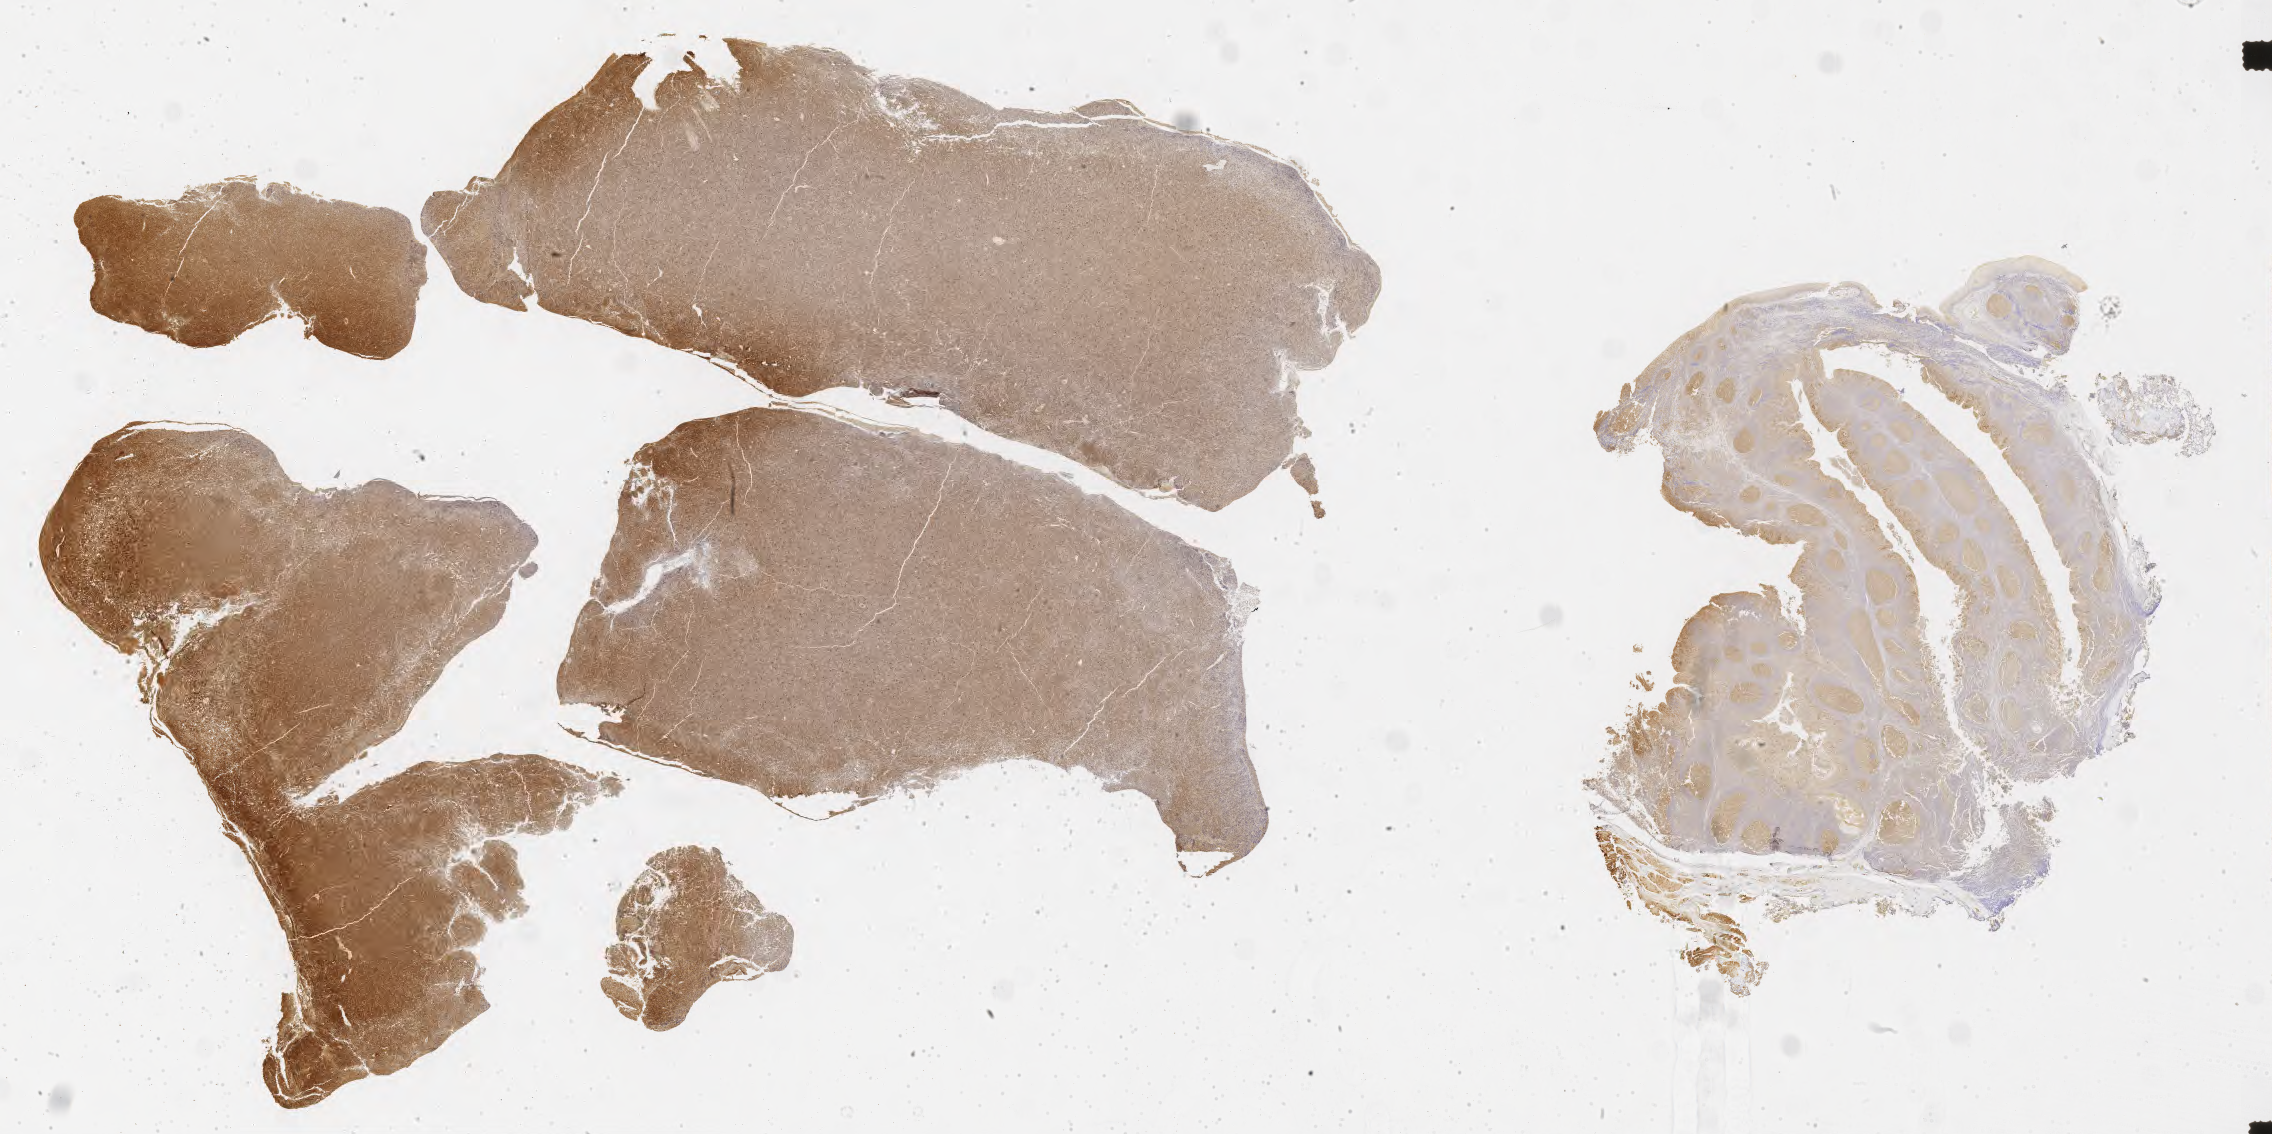
Immunohistochemistry (IHC) whole-slide image stained for BCL6 — low-resolution overview of the scanned area, about 36.7 x 18.3 mm. Specimen: tumor tissue. Site: peritoneum. Patient: female, age at initial diagnosis 7 years.
* diagnosis: Burkitt lymphoma, NOS